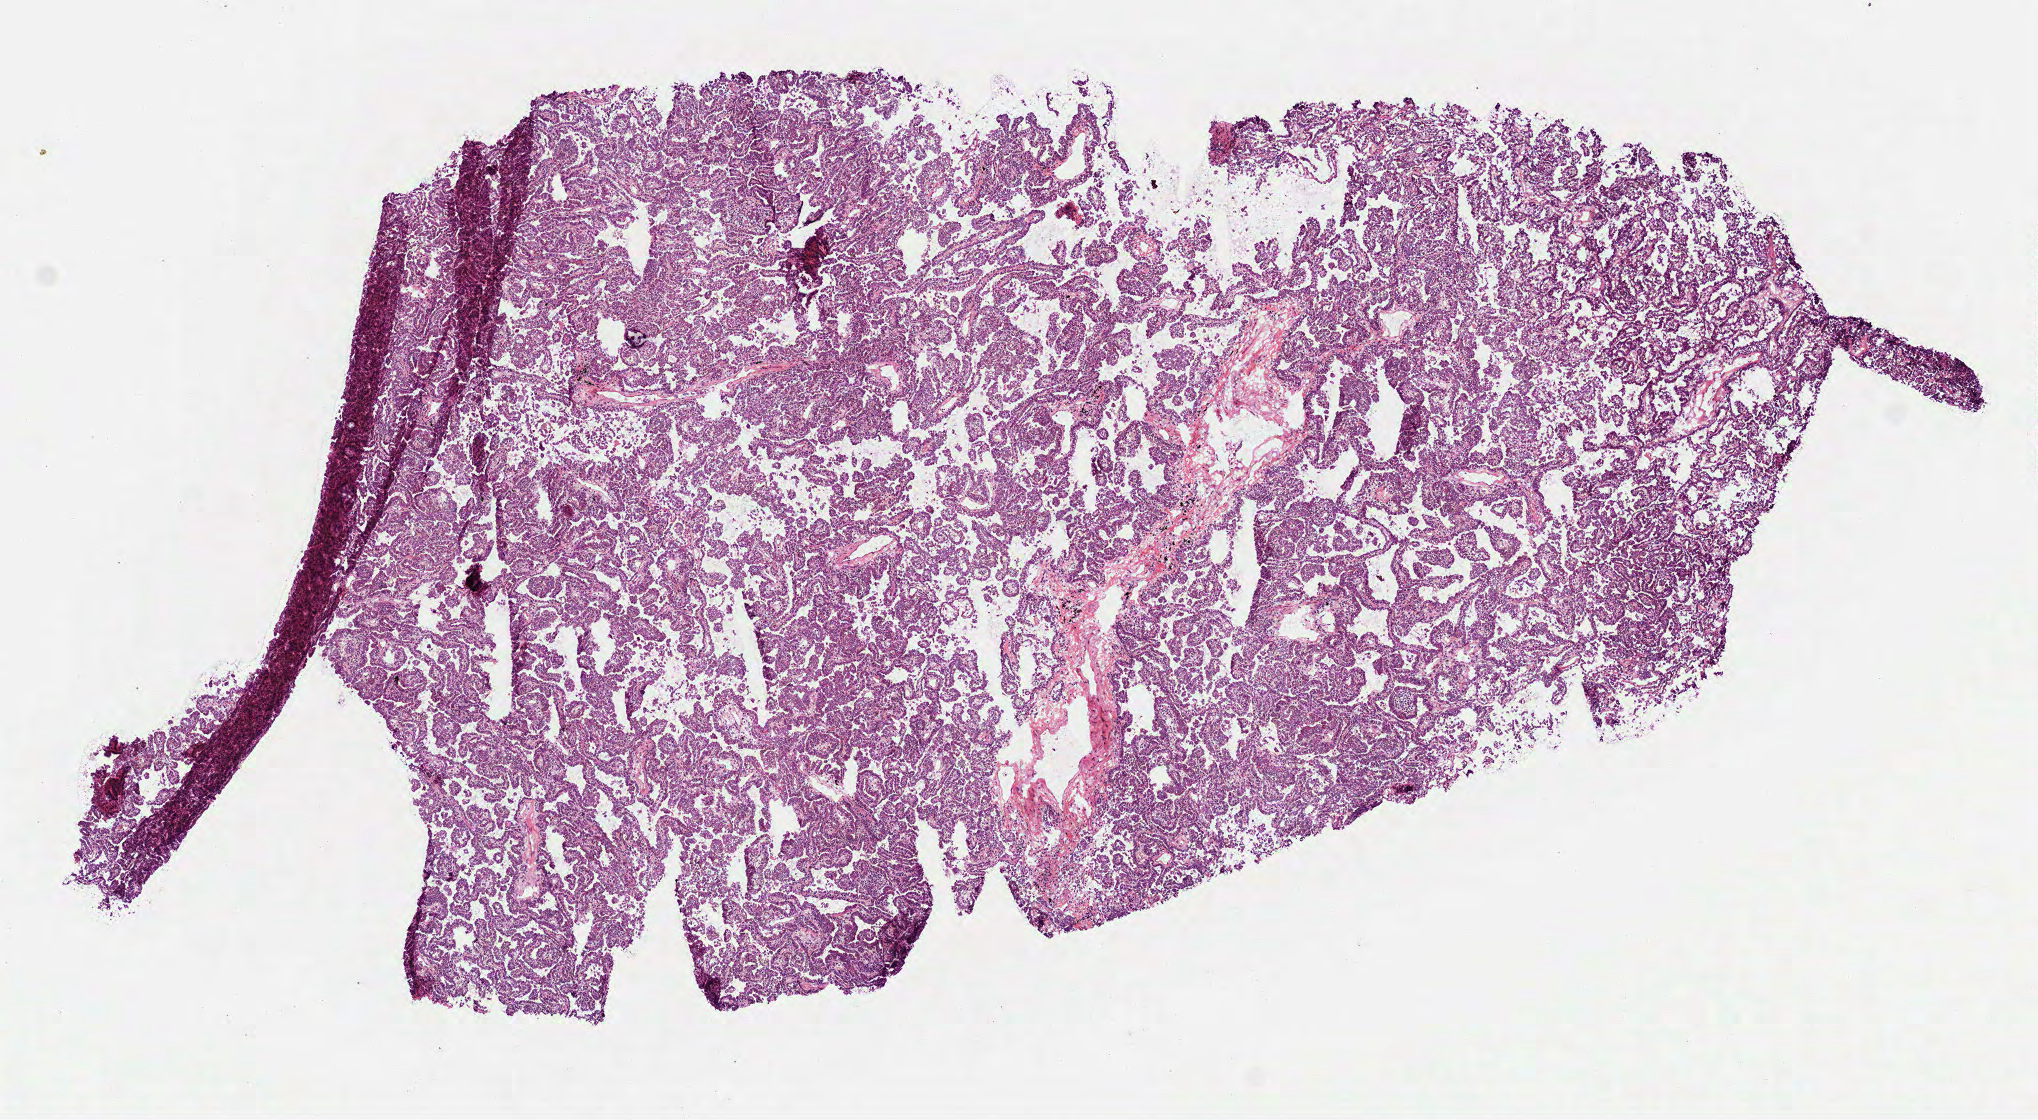
Whole-slide histology image, H&E, whole scanned area (about 8.2 x 4.5 mm, from a 40x scan) shown as a low-resolution overview, frozen section from the top of the tissue portion, primary tumour sample from the lung. Patient: male, age at initial diagnosis 62 years. Composition of this section per pathologist review: tumour cells 90%, tumour nuclei 80%, normal cells 0%, stromal cells 10%, necrosis 0%.
AJCC pathologic stage: IV (6th edition). Pathologic diagnosis: Adenocarcinoma with mixed subtypes.